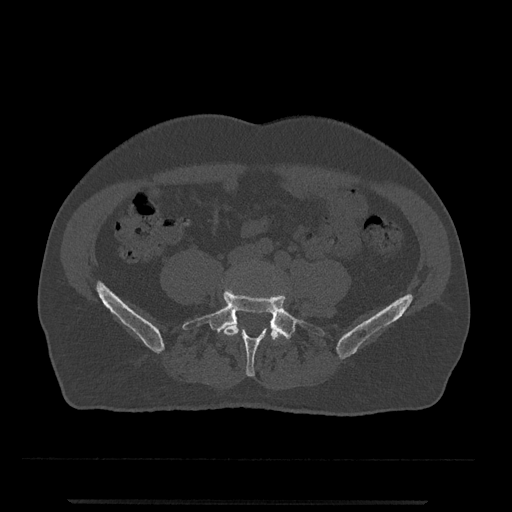
CT including the spine, one axial slice; position 89 of 797 along the scan axis; 120 kVp; bone window (W 1800 / L 400 HU); 0.5 mm slice thickness; 512 × 512 image matrix, field of view 419 × 419 mm. Male patient, age 63 years. Case-level facts recorded for this patient, not image findings: primary cancer: prostate.
Annotated regions visible in this slice (semi-automatically segmented with operator editing):
- L4 vertebra: box from (x=222, y=319) to (x=281, y=344) px
- L5 vertebra: (x=182, y=287)–(x=325, y=377)